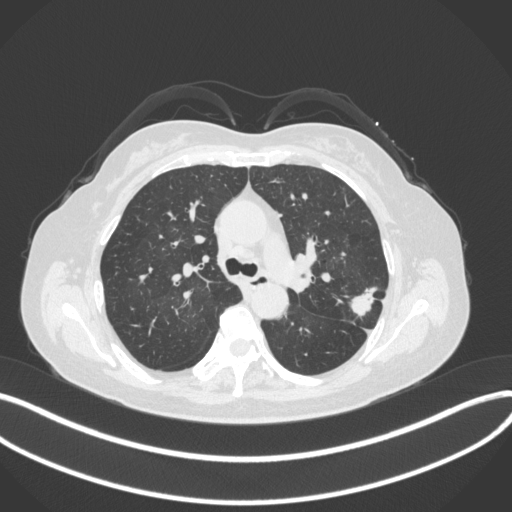
Chest CT, one axial slice. Slice 223 of 330 in the series (ordered by position). 120 kVp. Lung window (W 1500 / L -600 HU). 1 mm slice thickness. 512 × 512 image matrix, field of view 400 × 400 mm. Patient: female, 60 years. From the clinical record (not read from this slice): clinical TNM (as recorded): T1c N0 M0.
Outlined on this slice (rectangle marked by the reading radiologist):
- lung tumour (recorded histology: adenocarcinoma): bounding box <345,278,376,322> (left, top, right, bottom; pixels)